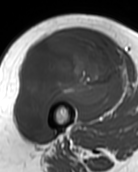
MRI of an extremity soft-tissue mass, one axial slice. Slice 59 of 99 in the series (ordered by position). MR volume resampled by the dataset authors to the PET/CT grid (not the native acquisition matrix). 138 × 172 image matrix. Female patient. From the clinical record (not read from this slice): histological type: pleiomorphic undifferentiated sarcoma; grade: high; site of the primary tumour: right quadricep.
Annotated regions visible in this slice (expert contour drawn on MRI and transferred to this co-registered scan by the dataset authors):
- gross tumour volume including surrounding oedema: bounding box <16,34,122,133> (left, top, right, bottom; pixels)
- gross tumour volume (mass): <16,34,122,133>